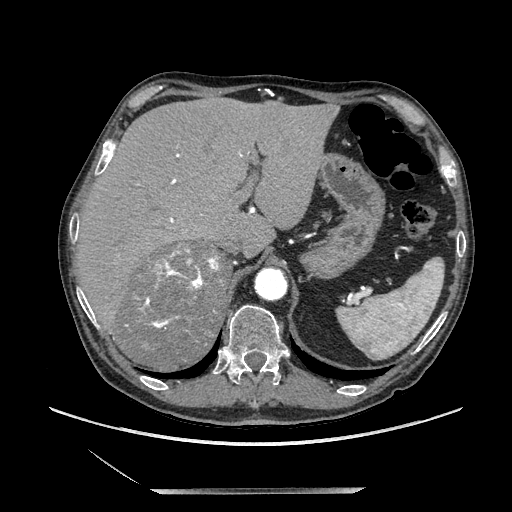
Contrast-enhanced abdominal CT, one axial slice. Position 158 of 243 along the scan axis. Soft-tissue window (W 400 / L 40 HU). 512 × 512 image matrix. Male patient. Case-level facts recorded for this patient, not image findings: diagnosis: adrenocortical carcinoma; tumour side: right adrenal; tumour size at pathology: 16 cm; Ki-67 index: 17 %.
Outlined on this slice (semi-automatically segmented with operator editing):
- mass: box from (x=121, y=243) to (x=229, y=371) px